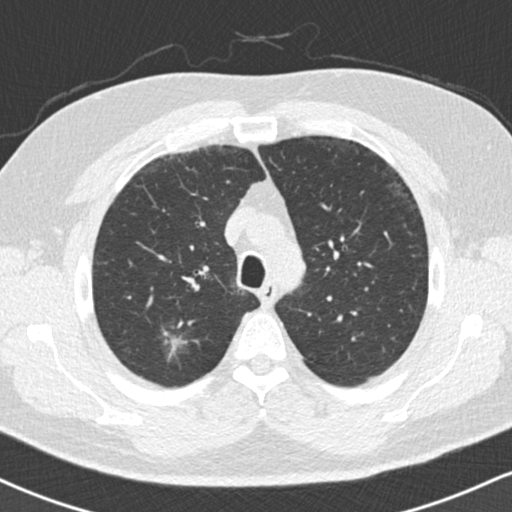
Axial slice from a low-dose chest CT screening exam. Second screening round (one year after baseline). Lung window (W 1500 / L -600 HU). 2 mm slice thickness. Standard (soft-tissue) reconstruction kernel (B30f). Male, age 59 years at enrolment.
Expert-annotated lung lesion, bounding box (x1, y1, x2, y2) in pixels: (152, 307, 205, 362). Reader record for this screening exam (exam-level; its link to the box is not recorded): non-calcified nodule or mass ≥4 mm, right upper lobe, 18 × 16 mm, ground glass attenuation, pre-existing on the prior screen: yes. Participant outcome: lung cancer diagnosed 60 days after this screen — bronchiolo-alveolar adenocarcinoma, NOS, right lower lobe, stage IA (AJCC 6th edition), 15 mm at pathology.